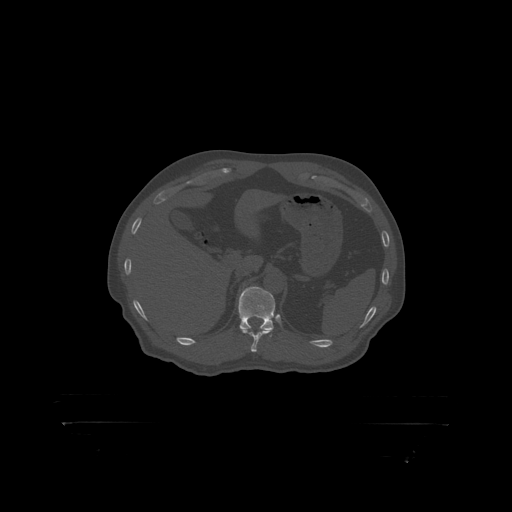
CT including the spine, one axial slice; position 365 of 399 along the scan axis; reconstruction kernel STANDARD; 120 kVp; bone window (W 1800 / L 400 HU); 1.25 mm slice thickness; 512 × 512 image matrix, field of view 650 × 650 mm. Male patient, age 46 years. From the clinical record (not read from this slice): primary cancer: skin.
Structures marked on this image (semi-automatic segmentation, software-assisted and operator-edited):
- T12 vertebra: box from (x=239, y=287) to (x=279, y=319) px